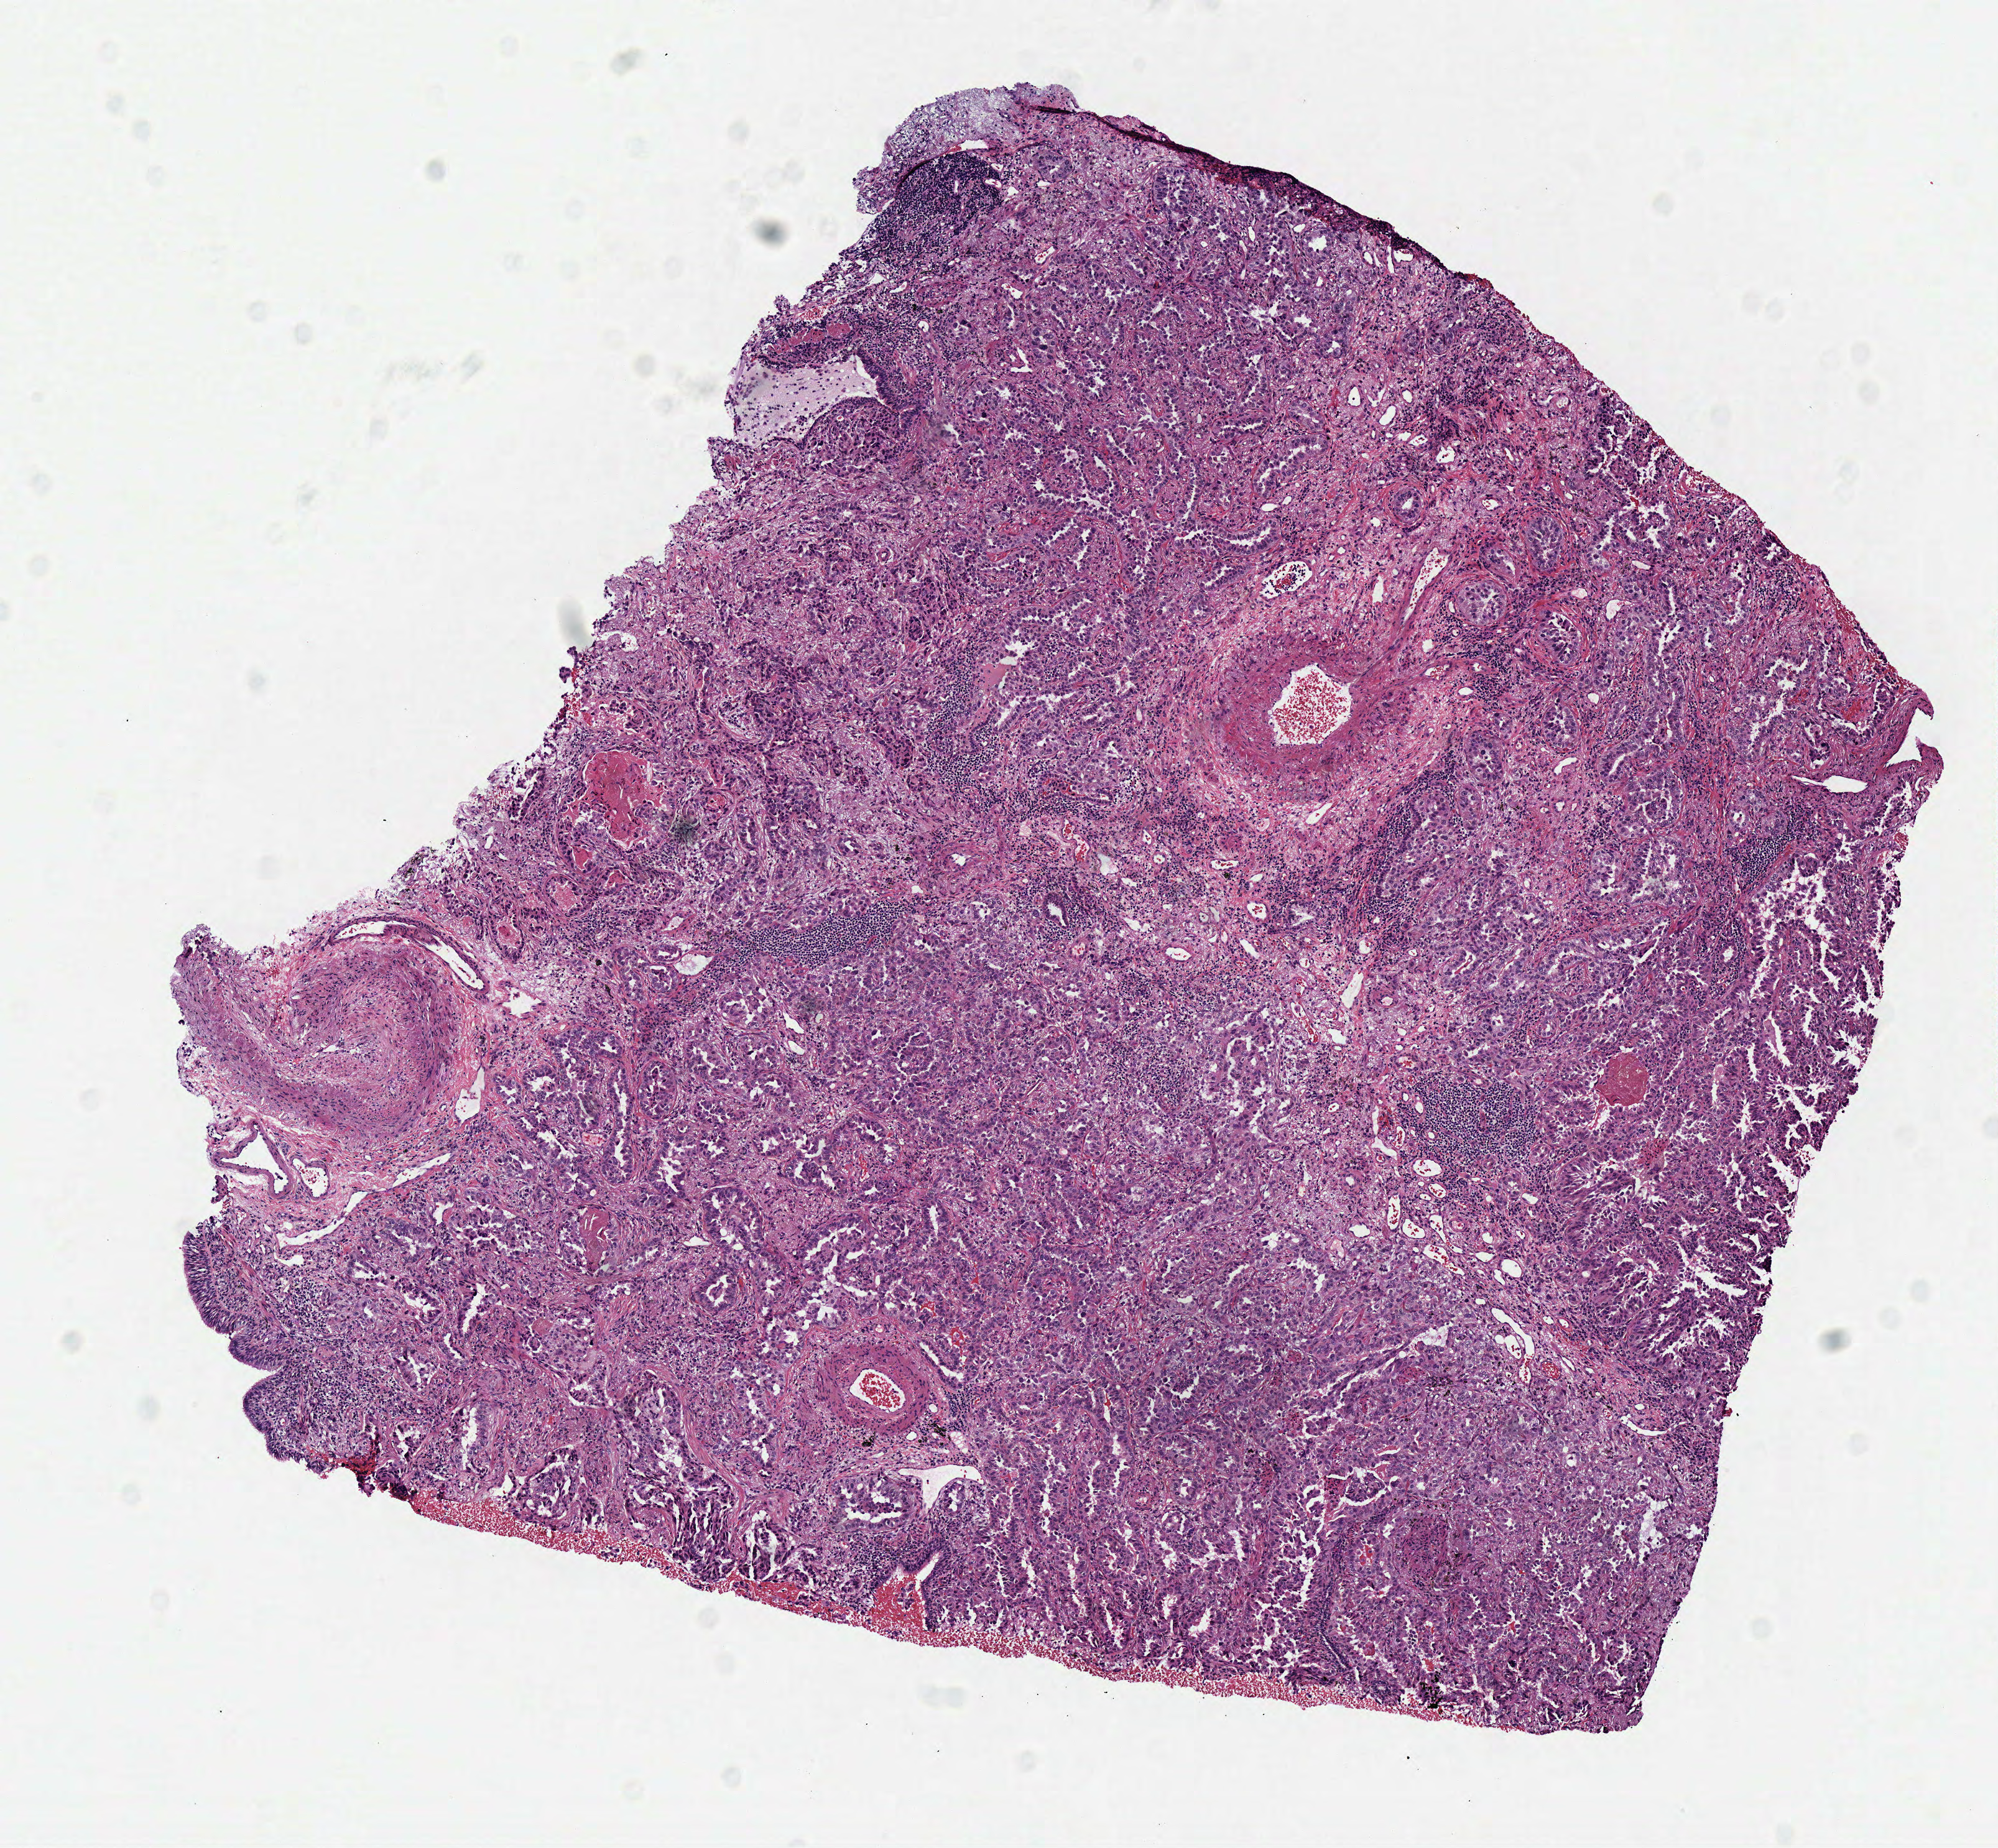
Hematoxylin and eosin (H&E) stained whole-slide image — low-resolution overview of the scanned area, about 6.3 x 5.9 mm (acquisition: 40x scan), frozen section from the top of the tissue portion, sample: primary tumour, lung. Patient: female, age at initial diagnosis 67 years. Pathologist review of this section (percent, as recorded): tumour cells 100%, tumour nuclei 90%, normal cells 0%, stromal cells 0%, necrosis 0%. Infiltration values recorded for this section: lymphocyte infiltration 2%, monocyte infiltration 0%, neutrophil infiltration 0%.
* AJCC pathologic stage: IA (7th edition)
* pathologic diagnosis: Adenocarcinoma, NOS (upper lobe, lung)